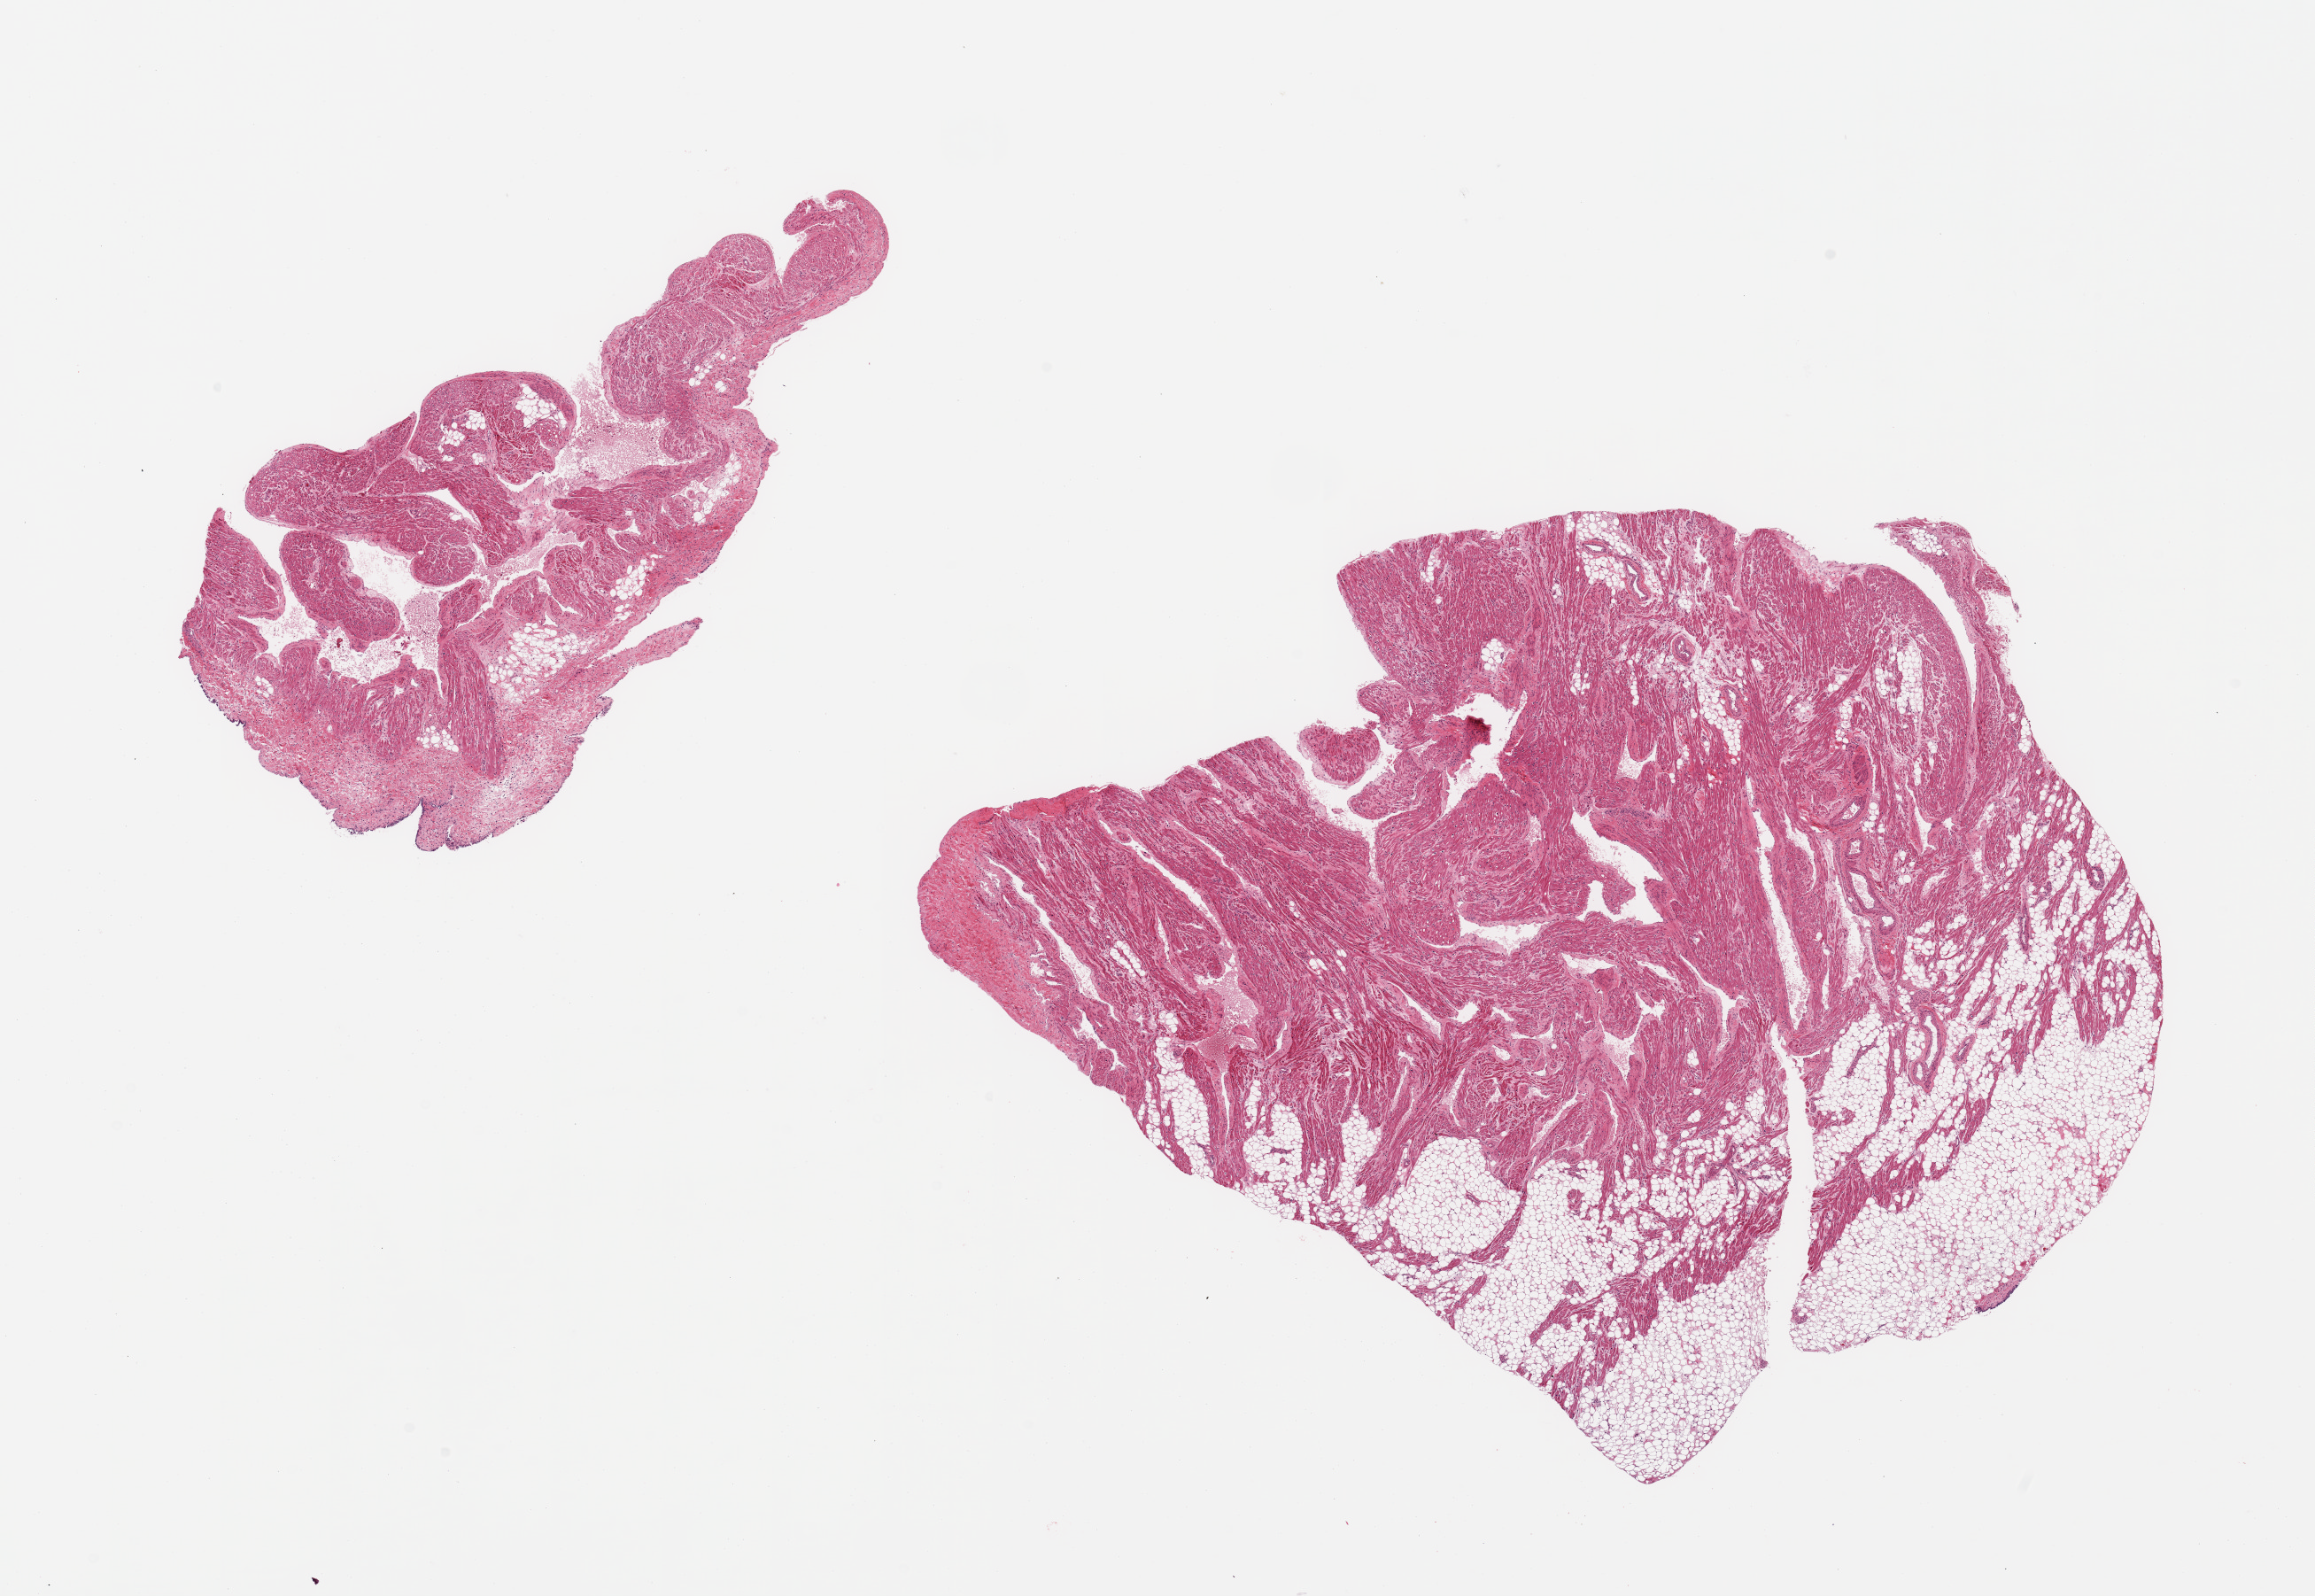
Hematoxylin and eosin (H&E) whole-slide image — shown as a low-resolution overview of the whole scanned area (about 20.7 x 14.3 mm); PAXgene-fixed paraffin-embedded (PFPE) section; section of auricular appendage (target tissue); tissue donor sample.
- pathologist's review note for this sample: 2 pieces; one with ~15% internal fat and other with ~30% external fat